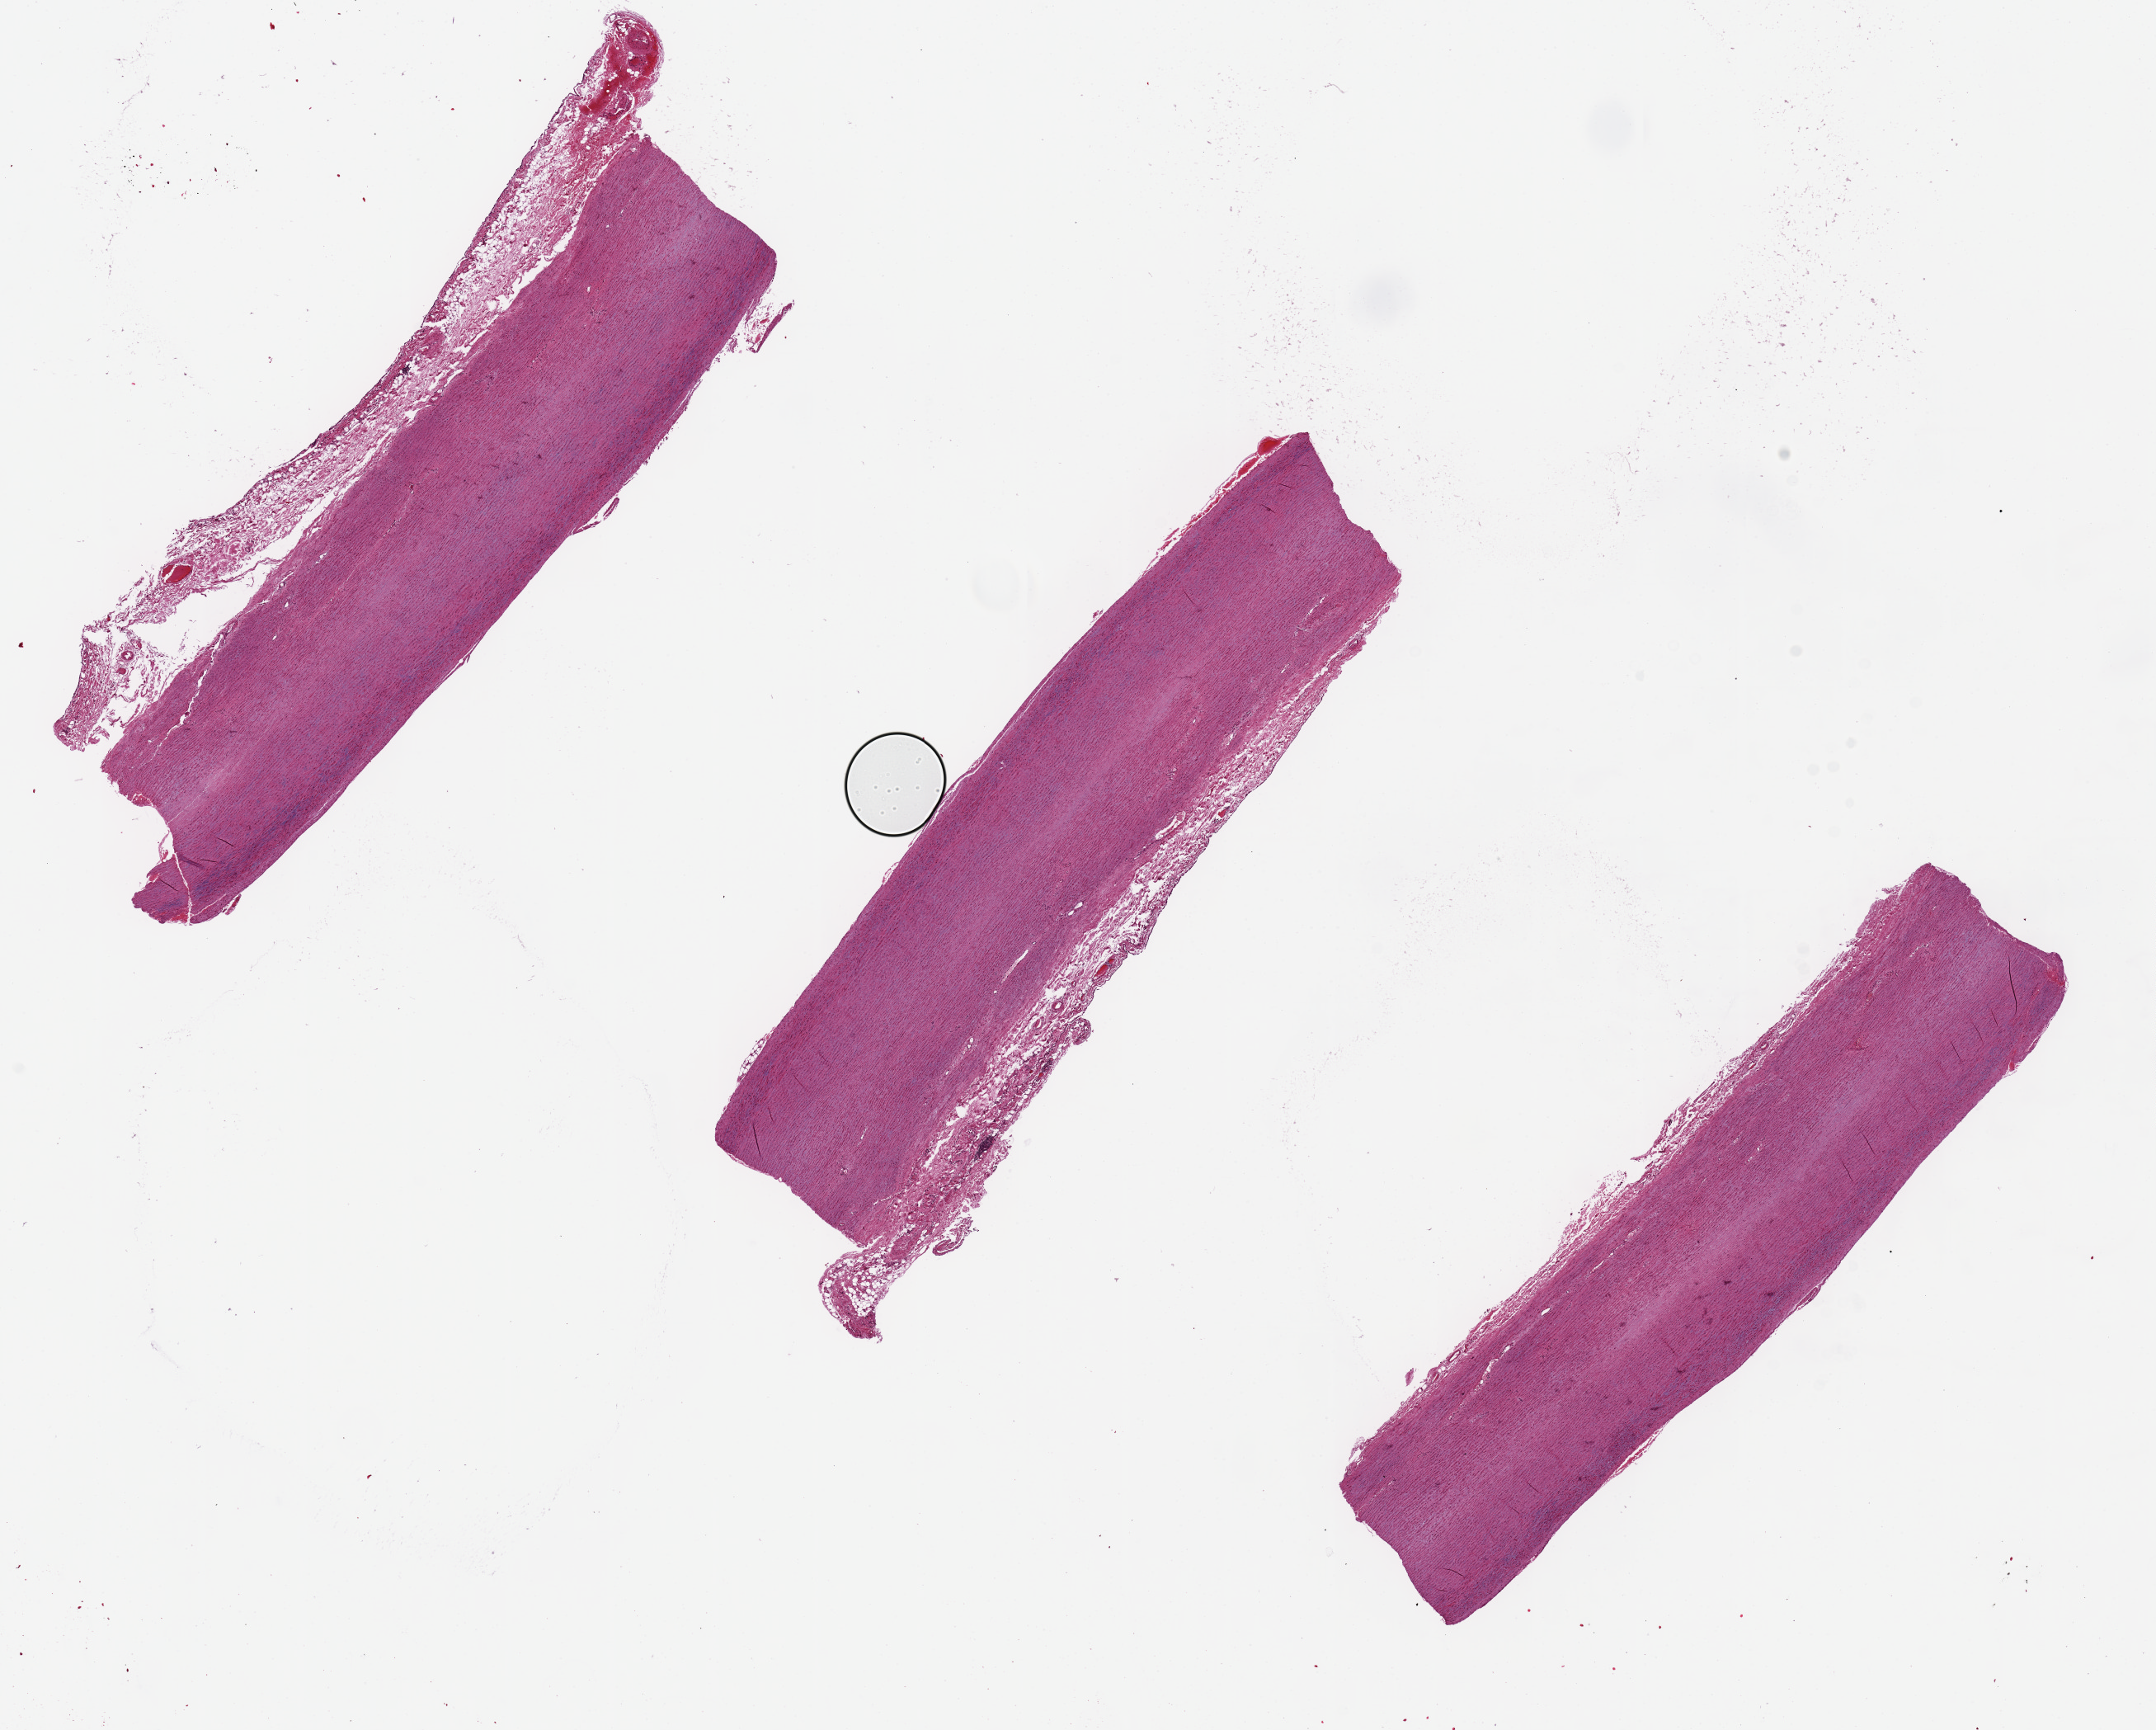
Hematoxylin and eosin (H&E) whole-slide image — low-resolution overview of the scanned area, about 20.7 x 16.6 mm, PAXgene-fixed, paraffin-embedded tissue, sampled site (target tissue): aorta, donor tissue sample. Donor sex: female.
• reviewer comment on this tissue sample: 3 pieces